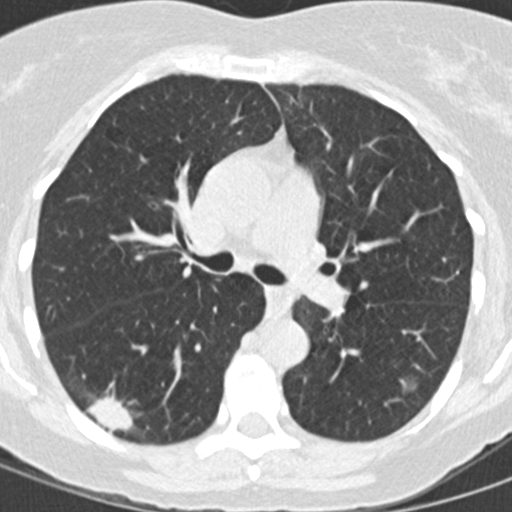
Low-dose screening chest CT, one axial slice; position 88 of 146 along the scan axis; reconstruction kernel B30f; 120 kVp; lung window (W 1500 / L -600 HU); 2 mm slice thickness; 512 × 512 image matrix, field of view 270 × 270 mm.
Outlined on this slice (expert manual segmentation):
- lesion 1 (tumor, lower lobe of right lung): box from (x=87, y=394) to (x=133, y=432) px